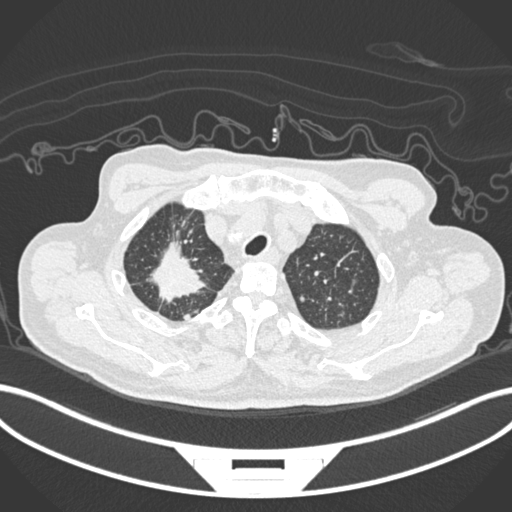
Chest CT, one axial slice. Slice 186 of 207 in the series (ordered by position). 120 kVp. Lung window (W 1500 / L -600 HU). 512 × 512 image matrix. Male patient, age 69 years. From the clinical record (not read from this slice): clinical TNM (as recorded): T1c N1 M1.
Structures marked on this image (rectangle marked by the reading radiologist):
- lung tumour (recorded histology: adenocarcinoma): bounding box <145,234,209,304> (left, top, right, bottom; pixels)